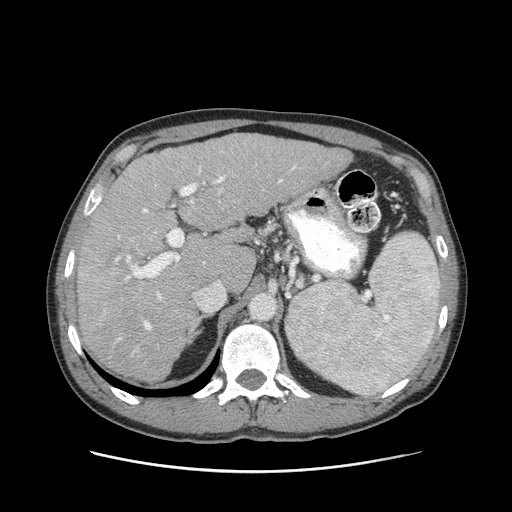
Contrast-enhanced abdominal CT (liver protocol), one axial slice. Slice 62 of 93 in the series (ordered by position). 120 kVp. Soft-tissue window (W 400 / L 40 HU). 2.5 mm slice thickness. 512 × 512 image matrix, field of view 380 × 380 mm. Case-level facts recorded for this patient, not image findings: diagnosis: hepatocellular carcinoma (patient treated with transarterial chemoembolisation; whether this scan precedes or follows treatment is not stated here); TNM stage (as recorded): Stage-II; Child-Pugh class: A; tumour size: 1 cm.
Outlined on this slice (semi-automatically segmented with operator editing):
- liver parenchyma outside the tumour (the mass and vessels are separate outlines, so this box may not span the whole liver): bounding box <78,134,352,380> (left, top, right, bottom; pixels)
- mass: <91,271,116,297>
- liver vessels: <115,165,296,340>